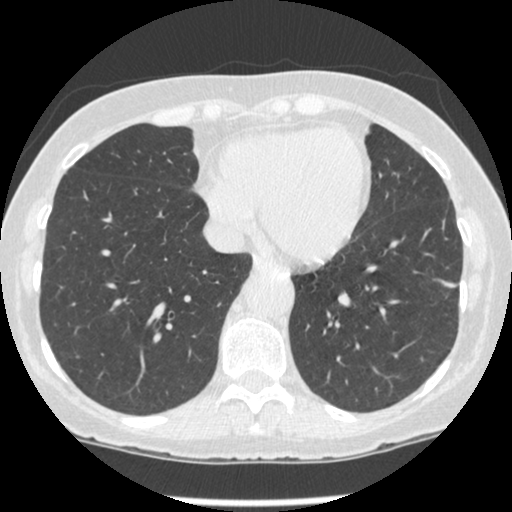
Low-dose screening chest CT, one axial slice; position 79 of 247 along the scan axis; 120 kVp; lung window (W 1500 / L -600 HU); 1.25 mm slice thickness; 512 × 512 image matrix.
Outlined on this slice (expert manual segmentation):
- lesion 1 (tumor, lower lobe of left lung): bounding box [x1, y1, x2, y2] px = [442, 281, 456, 288]